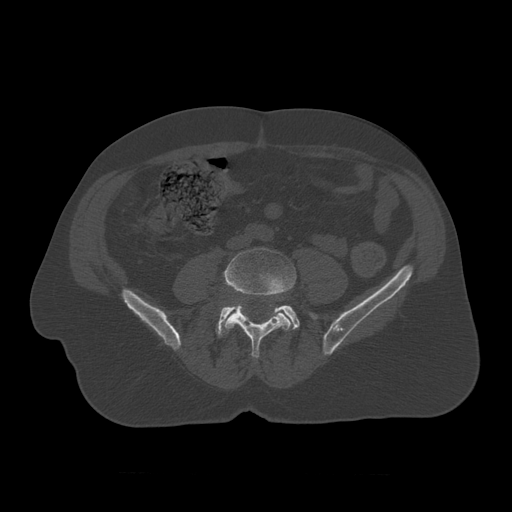
CT including the spine, one axial slice. Slice 269 of 450 in the series (ordered by position). Bone window (W 1800 / L 400 HU). 512 × 512 image matrix. Patient age 75 years. From the clinical record (not read from this slice): primary cancer: prostate.
Outlined on this slice (semi-automatic segmentation, software-assisted and operator-edited):
- L4 vertebra: bounding box [x1, y1, x2, y2] px = [223, 248, 297, 359]
- L5 vertebra: [216, 305, 318, 338]